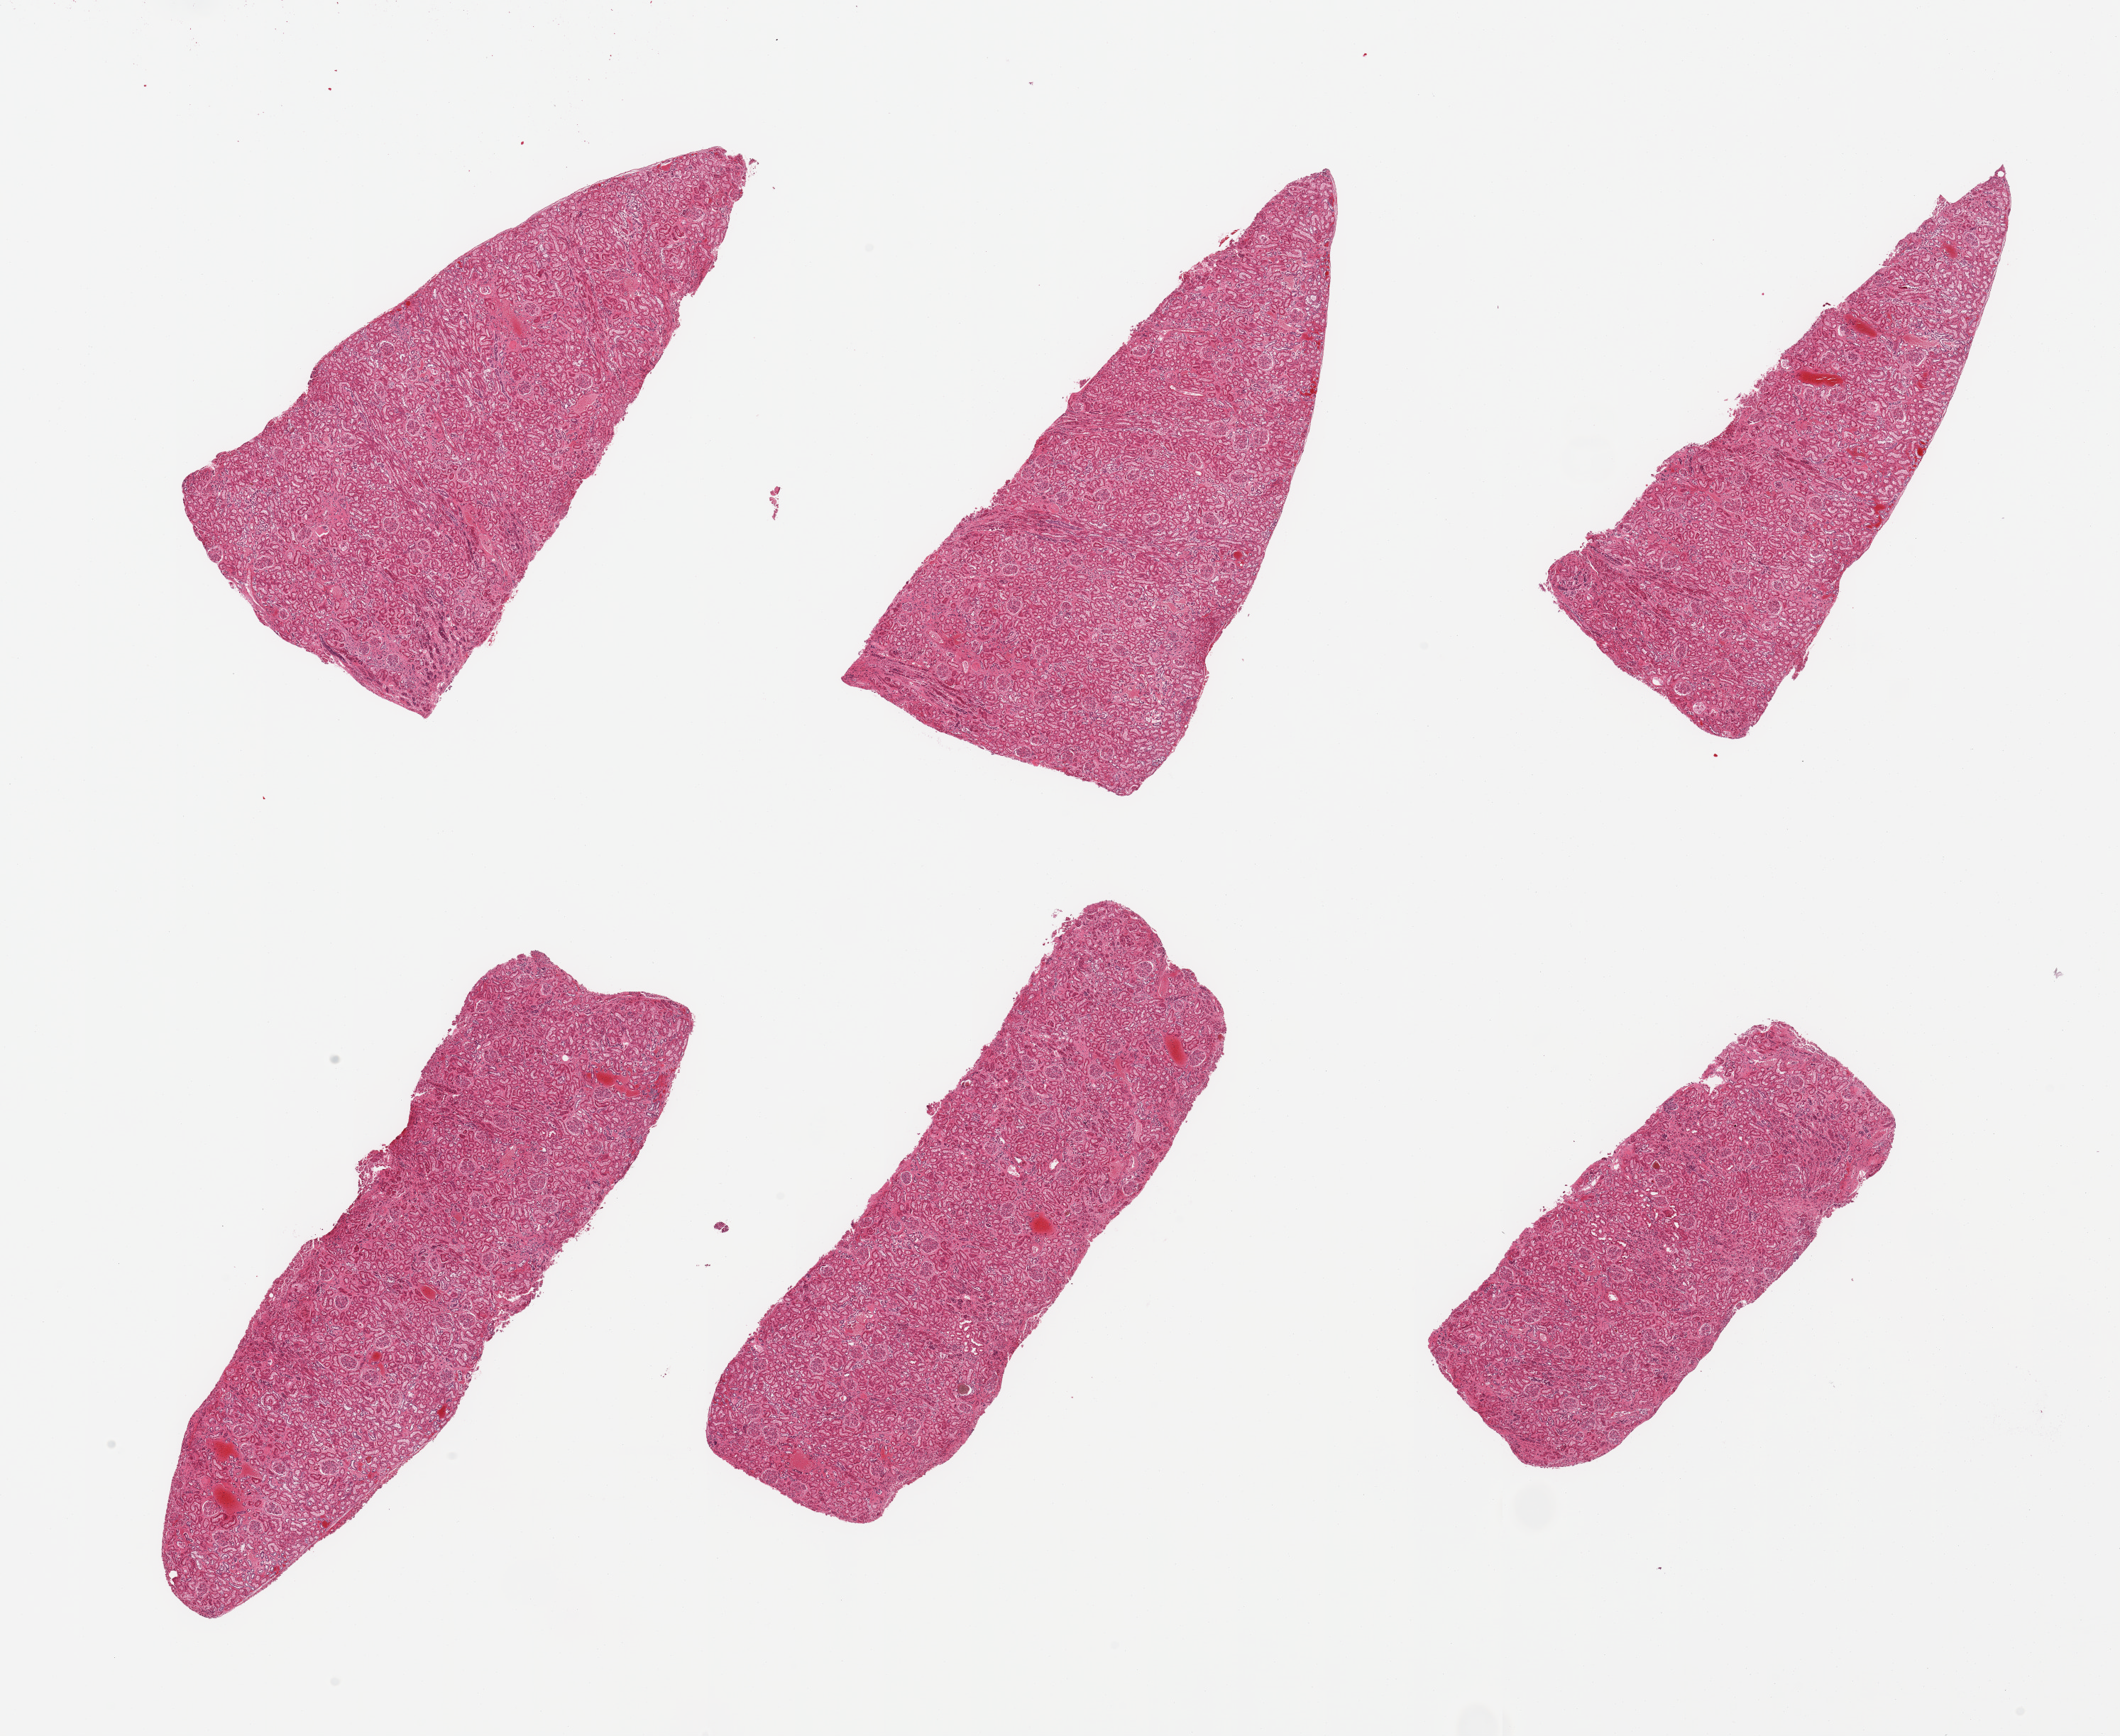
Haematoxylin and eosin whole-slide image, brightfield, shown as a low-resolution overview of the whole scanned area (about 23.6 x 19.3 mm, acquisition: 20x scan); PAXgene-fixed, paraffin-embedded tissue; target tissue: renal cortex; donor tissue sample. Donor sex: female.
Reviewer comment on this tissue sample: 6 pieces; no active or chronic renal or vascular lesions.